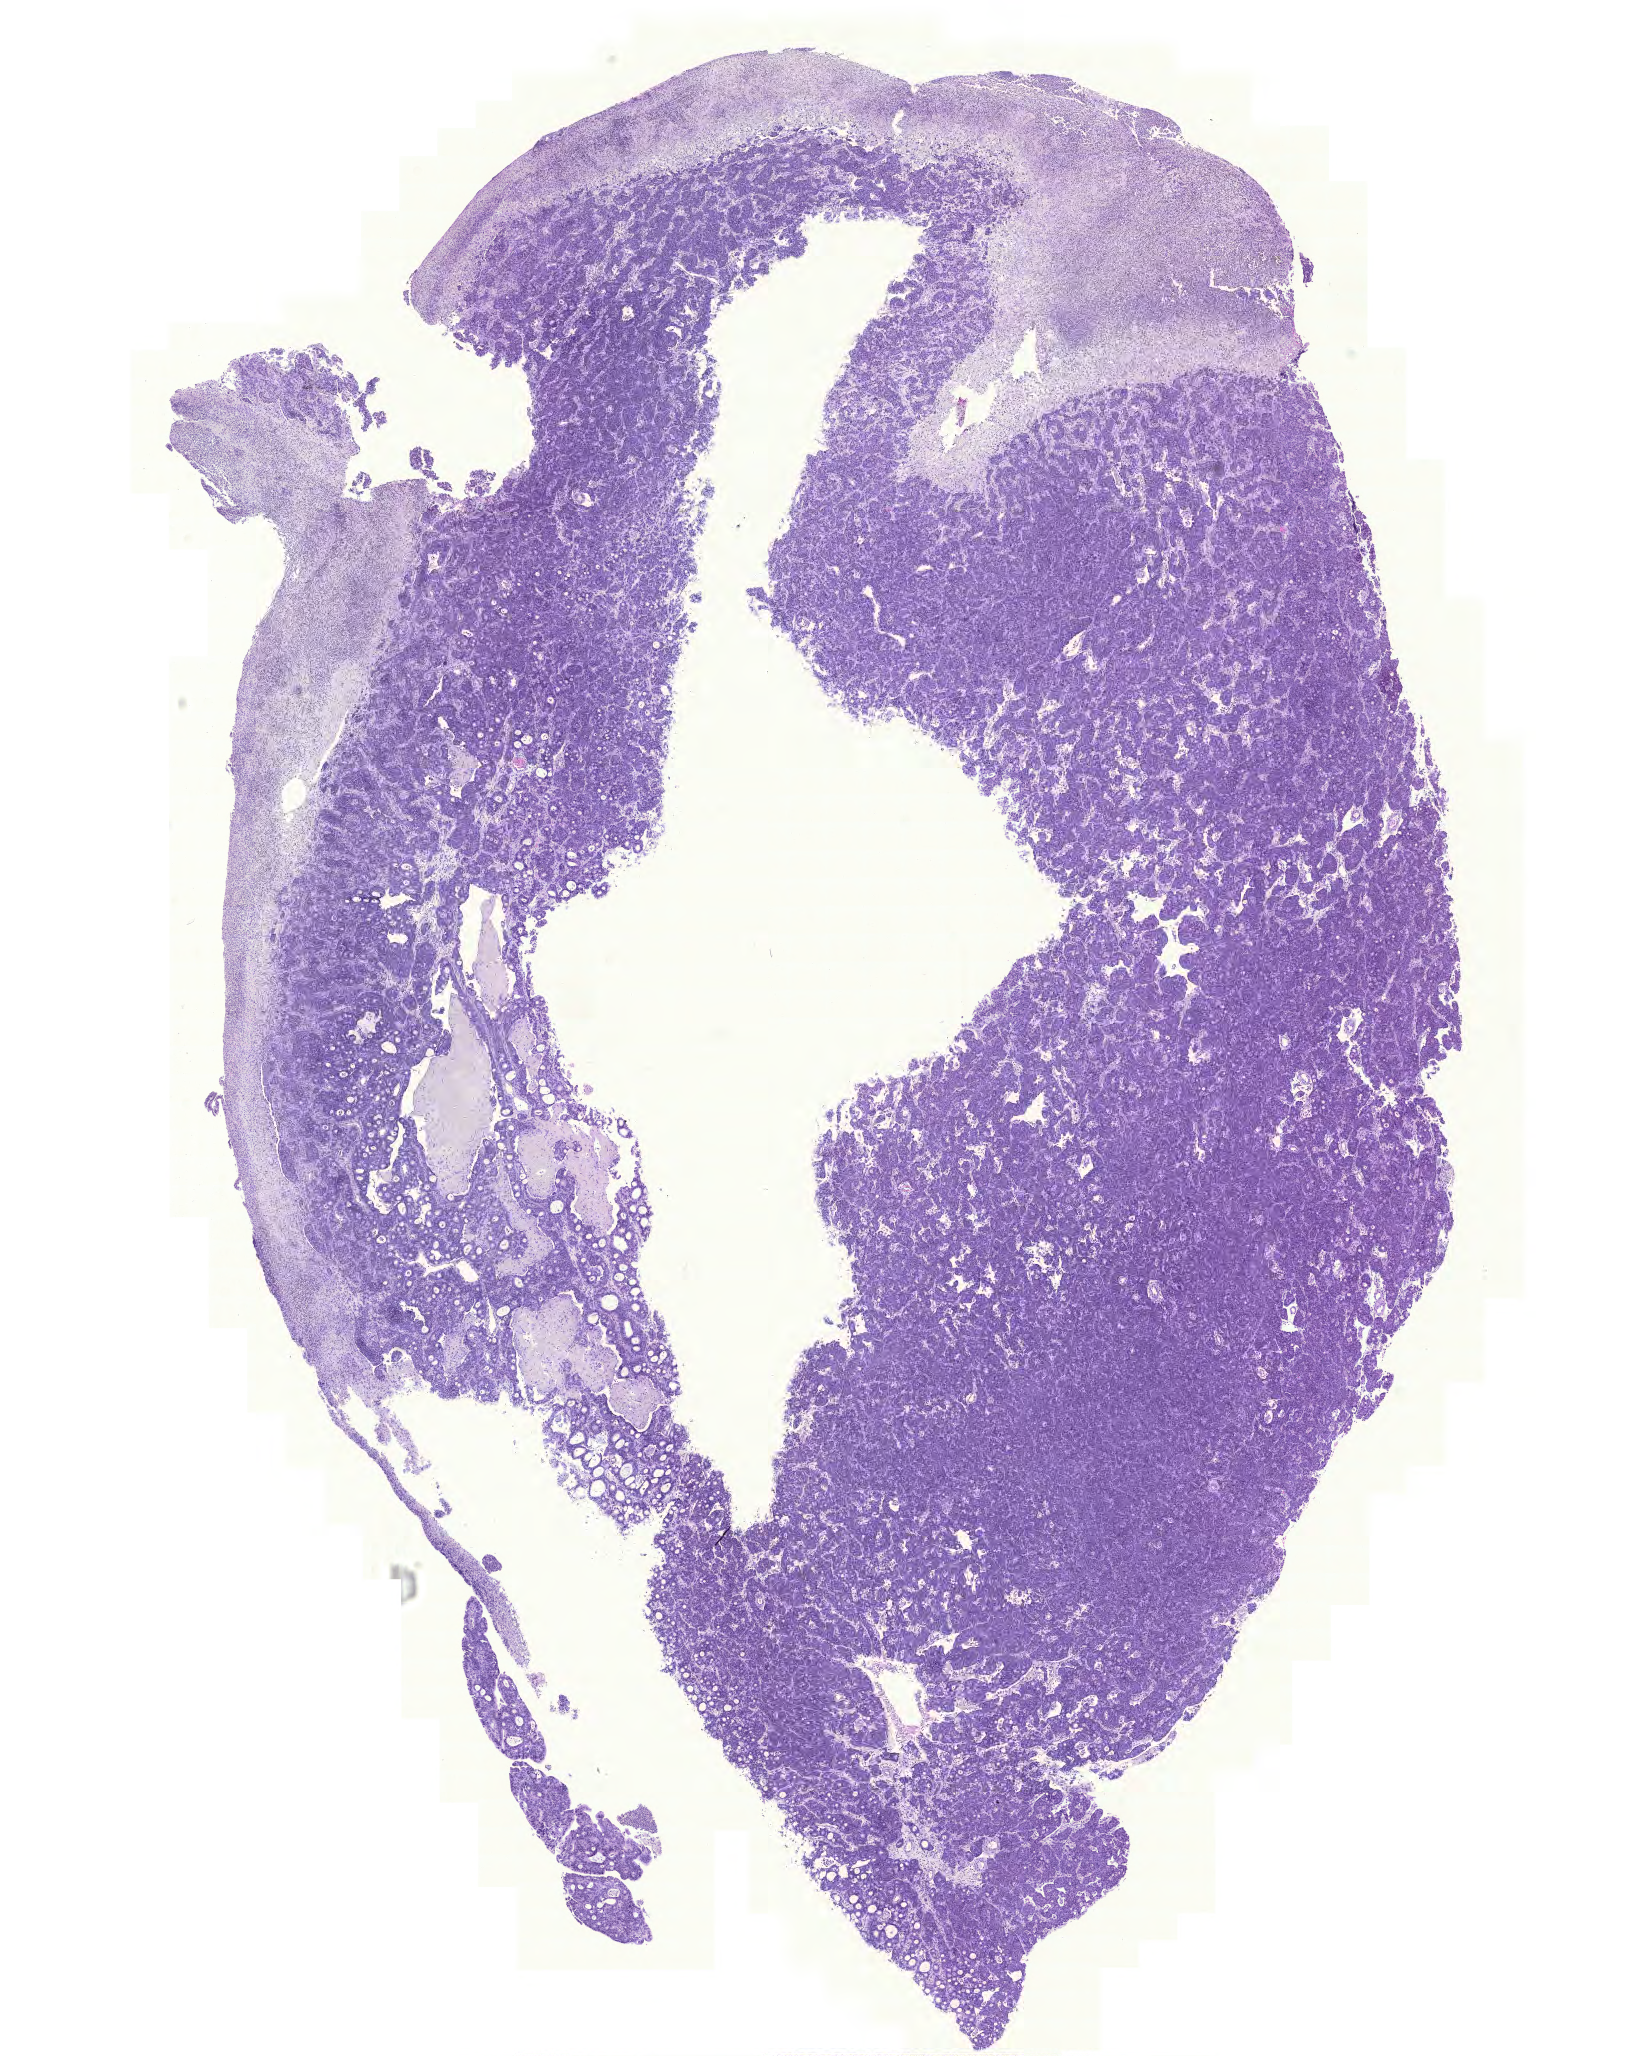
Digitized H&E tissue section (whole slide) — low-resolution overview of the scanned area, about 12.2 x 15.3 mm (acquisition: 20x scan); FFPE section; primary tumour sample from the stomach. Male, age 70 years at initial diagnosis. Histologic grade: G3 (poorly differentiated).
Lymph nodes positive (case pathology): 39 of 40 examined. AJCC pathologic stage: IV (6th edition). Histologic diagnosis: Adenocarcinoma, intestinal type.